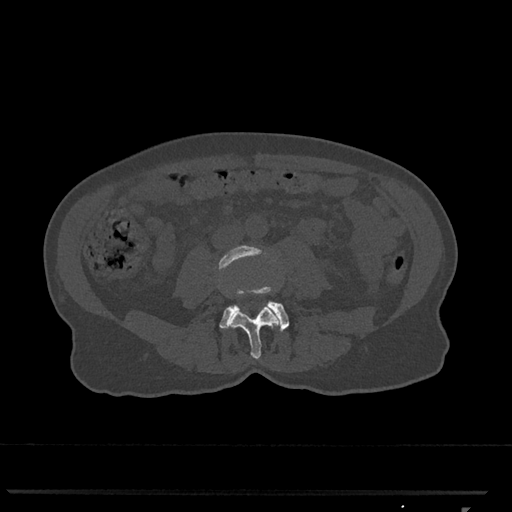
CT including the spine, one axial slice; slice 243 of 793 in the series (ordered by position); reconstruction kernel Br40s/3; 120 kVp; bone window (W 1800 / L 400 HU); 0.5 mm slice thickness; 512 × 512 image matrix. Patient: female, 62 years. Case-level facts recorded for this patient, not image findings: primary cancer: renal.
Outlined on this slice (semi-automatically segmented with operator editing):
- L3 vertebra: box from (x=219, y=245) to (x=281, y=359) px
- L4 vertebra: (x=219, y=287)–(x=289, y=331)